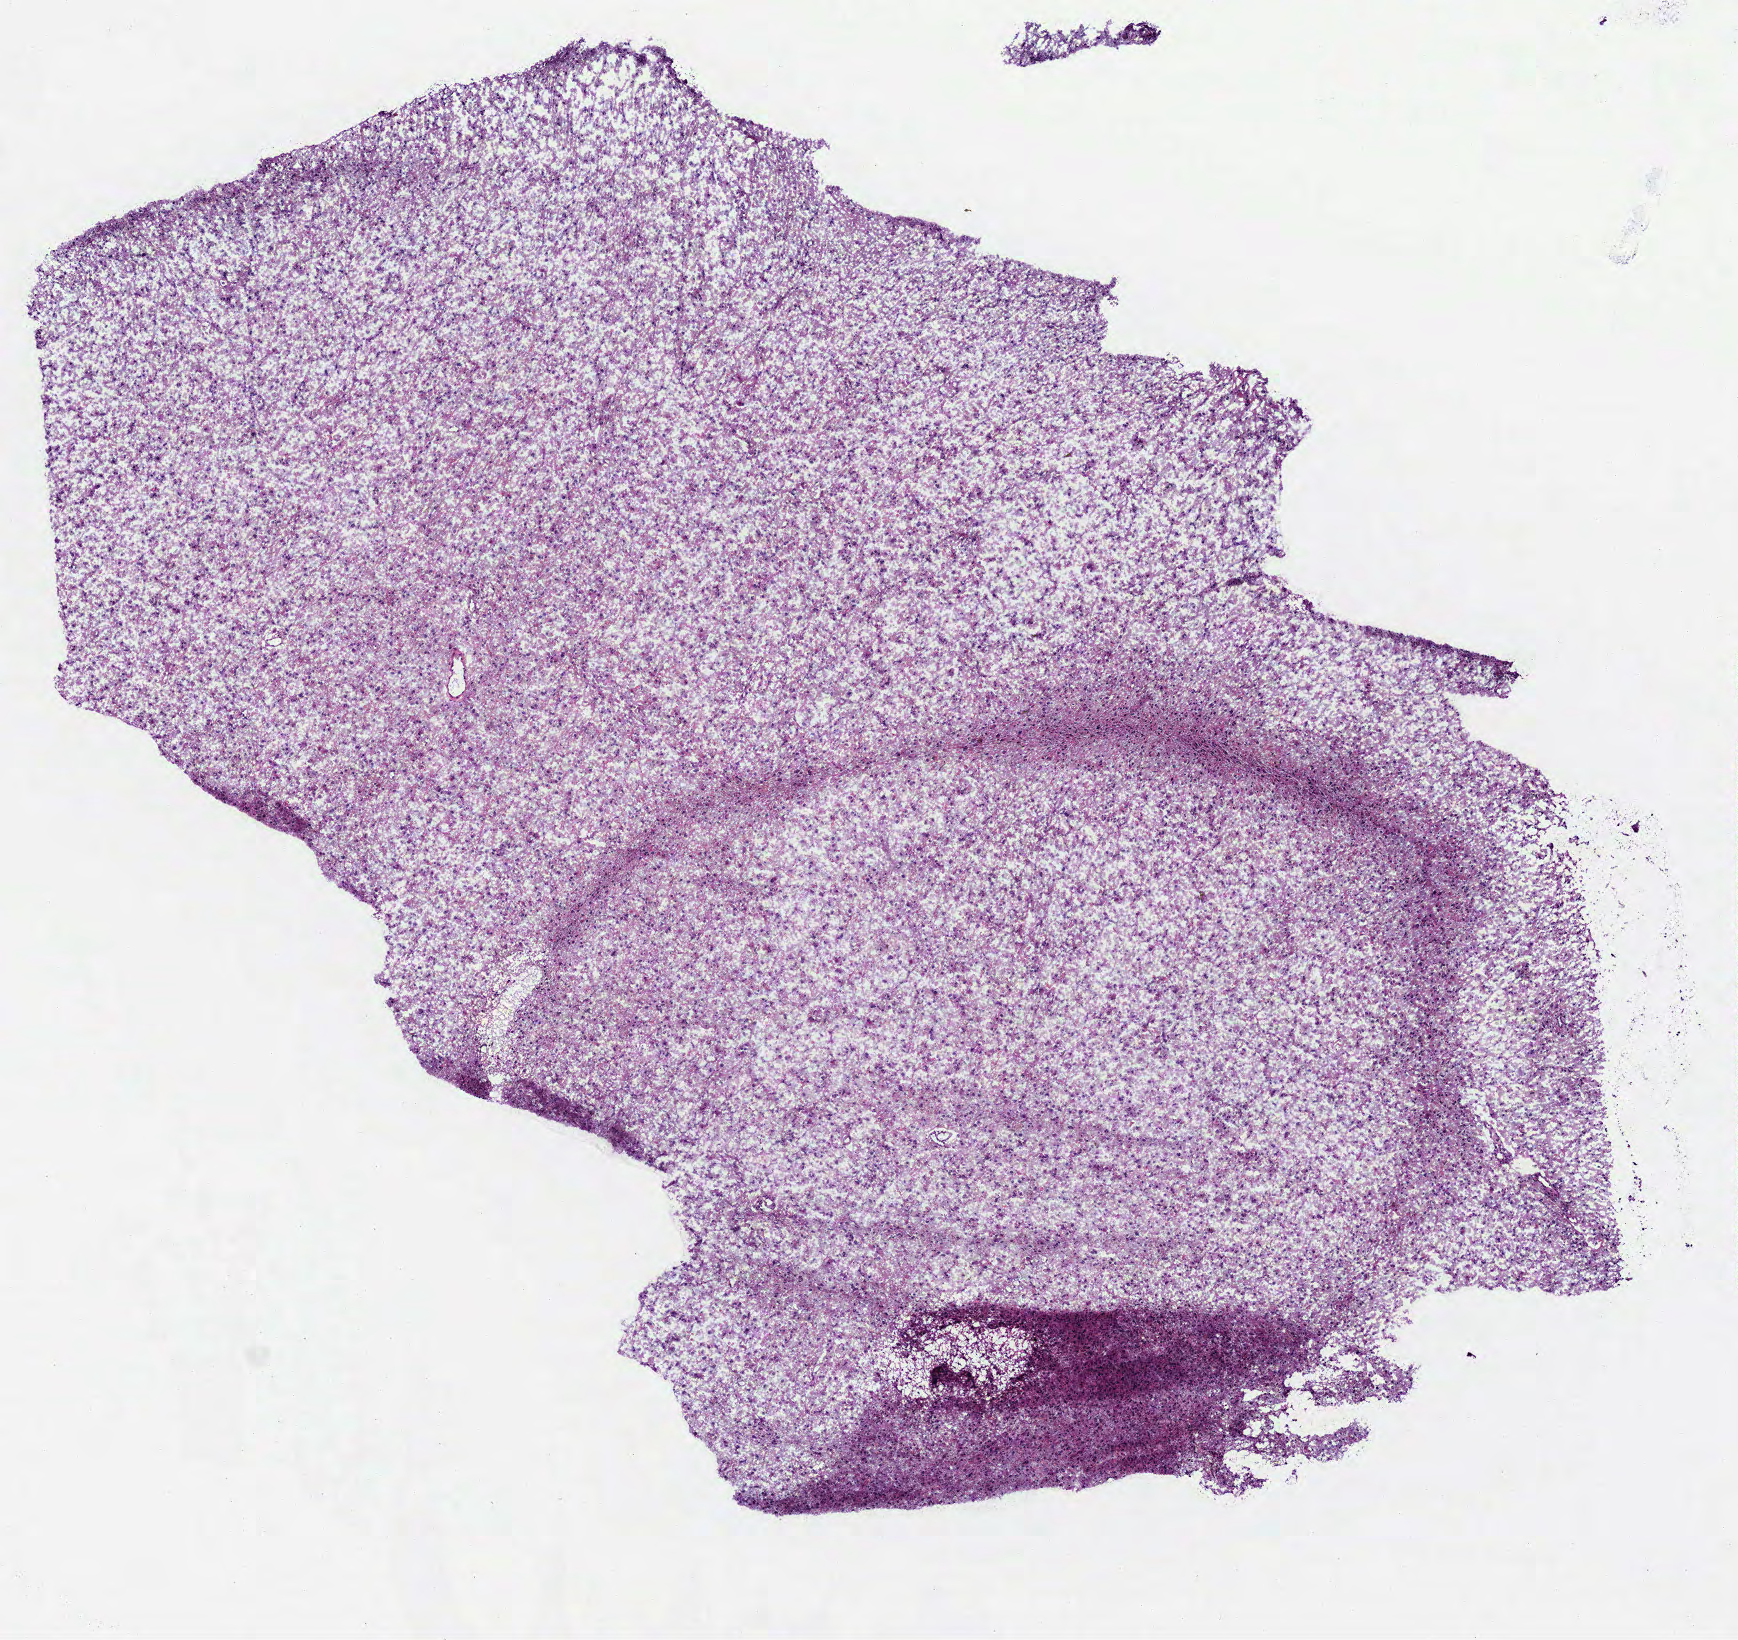
Digitized H&E-stained tissue section (whole slide) — low-resolution overview of the scanned area, about 7.0 x 6.6 mm, frozen section from the top of the tissue portion, brain, primary tumour sample. Male patient; age at initial diagnosis 31 years. Pathologist review of this section (percent, as recorded): tumour cells 100%, tumour nuclei 80%.
Diagnosis: Mixed glioma (cerebrum).